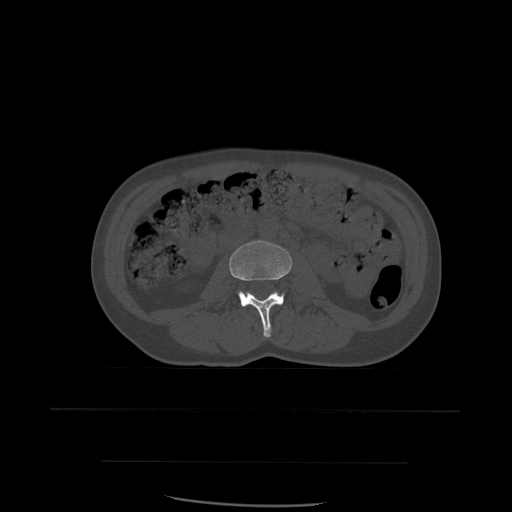
CT including the spine, one axial slice; position 195 of 574 along the scan axis; bone window (W 1800 / L 400 HU); 1.25 mm slice thickness; 512 × 512 image matrix, field of view 392 × 392 mm. Patient age 48 years. Case-level facts recorded for this patient, not image findings: primary cancer: lung; vertebrae with lytic lesions (as recorded): T11.
Outlined on this slice (semi-automatic segmentation, software-assisted and operator-edited):
- L3 vertebra: bounding box [x1, y1, x2, y2] px = [229, 241, 293, 338]